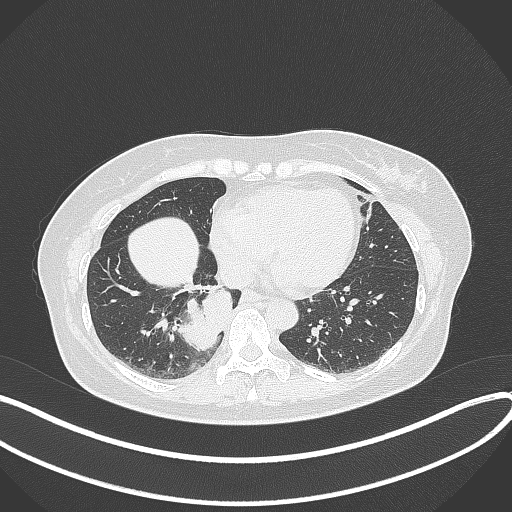
Chest CT, one axial slice. Position 117 of 331 along the scan axis. Lung window (W 1500 / L -600 HU). 1 mm slice thickness. 512 × 512 image matrix, field of view 400 × 400 mm. Patient: female, 54 years. Case-level facts recorded for this patient, not image findings: clinical TNM (as recorded): T4 N0 M0.
Outlined on this slice (rectangle marked by the reading radiologist):
- lung tumour (recorded histology: adenocarcinoma): bounding box [x1, y1, x2, y2] px = [166, 276, 239, 356]